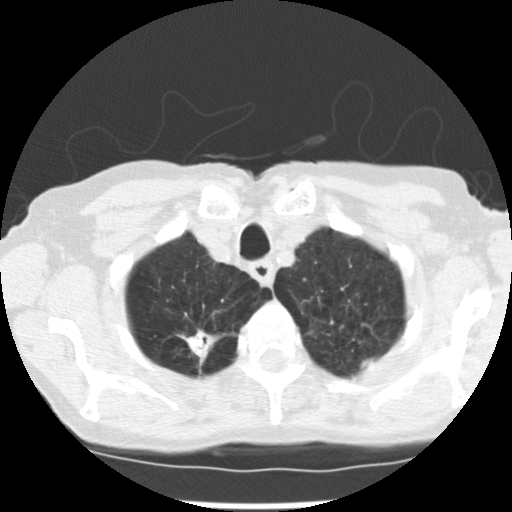
Axial slice from a low-dose chest CT screening exam. Baseline annual screen. Lung window (W 1500 / L -600 HU). 2.5 mm slice thickness. 120 kVp. Slice 28 of 265 in the series. Female, age 72 years at enrolment. Current smoker at enrolment.
Expert-annotated lung lesion, bounding box [x1, y1, x2, y2] px = [173, 315, 231, 359]. The screening reader recorded 3 non-calcified nodules or masses ≥4 mm on this exam; which of them this box marks is not recorded. Official screen result: positive, change unspecified: nodule(s) >= 4 mm or enlarging nodule(s), mass(es), or other non-specific abnormalities suspicious for lung cancer. Lung cancer was diagnosed 50 days after this screen: adenocarcinoma, NOS, right upper lobe, moderately differentiated (G2), stage IB (AJCC 6th edition), 22 mm at pathology.